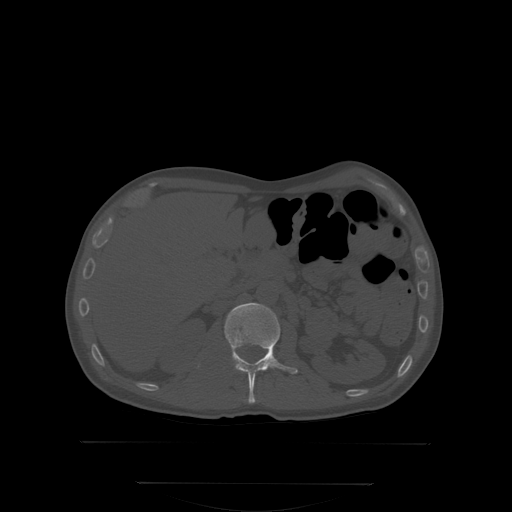
CT including the spine, one axial slice. Slice 152 of 350 in the series (ordered by position). Bone window (W 1800 / L 400 HU). 2.5 mm slice thickness. 512 × 512 image matrix. Male patient, age 58 years. From the clinical record (not read from this slice): primary cancer: prostate; vertebrae with lytic lesions (as recorded): L1.
Annotated regions visible in this slice (semi-automatic segmentation, software-assisted and operator-edited):
- L1 vertebra: bounding box <224,304,299,403> (left, top, right, bottom; pixels)